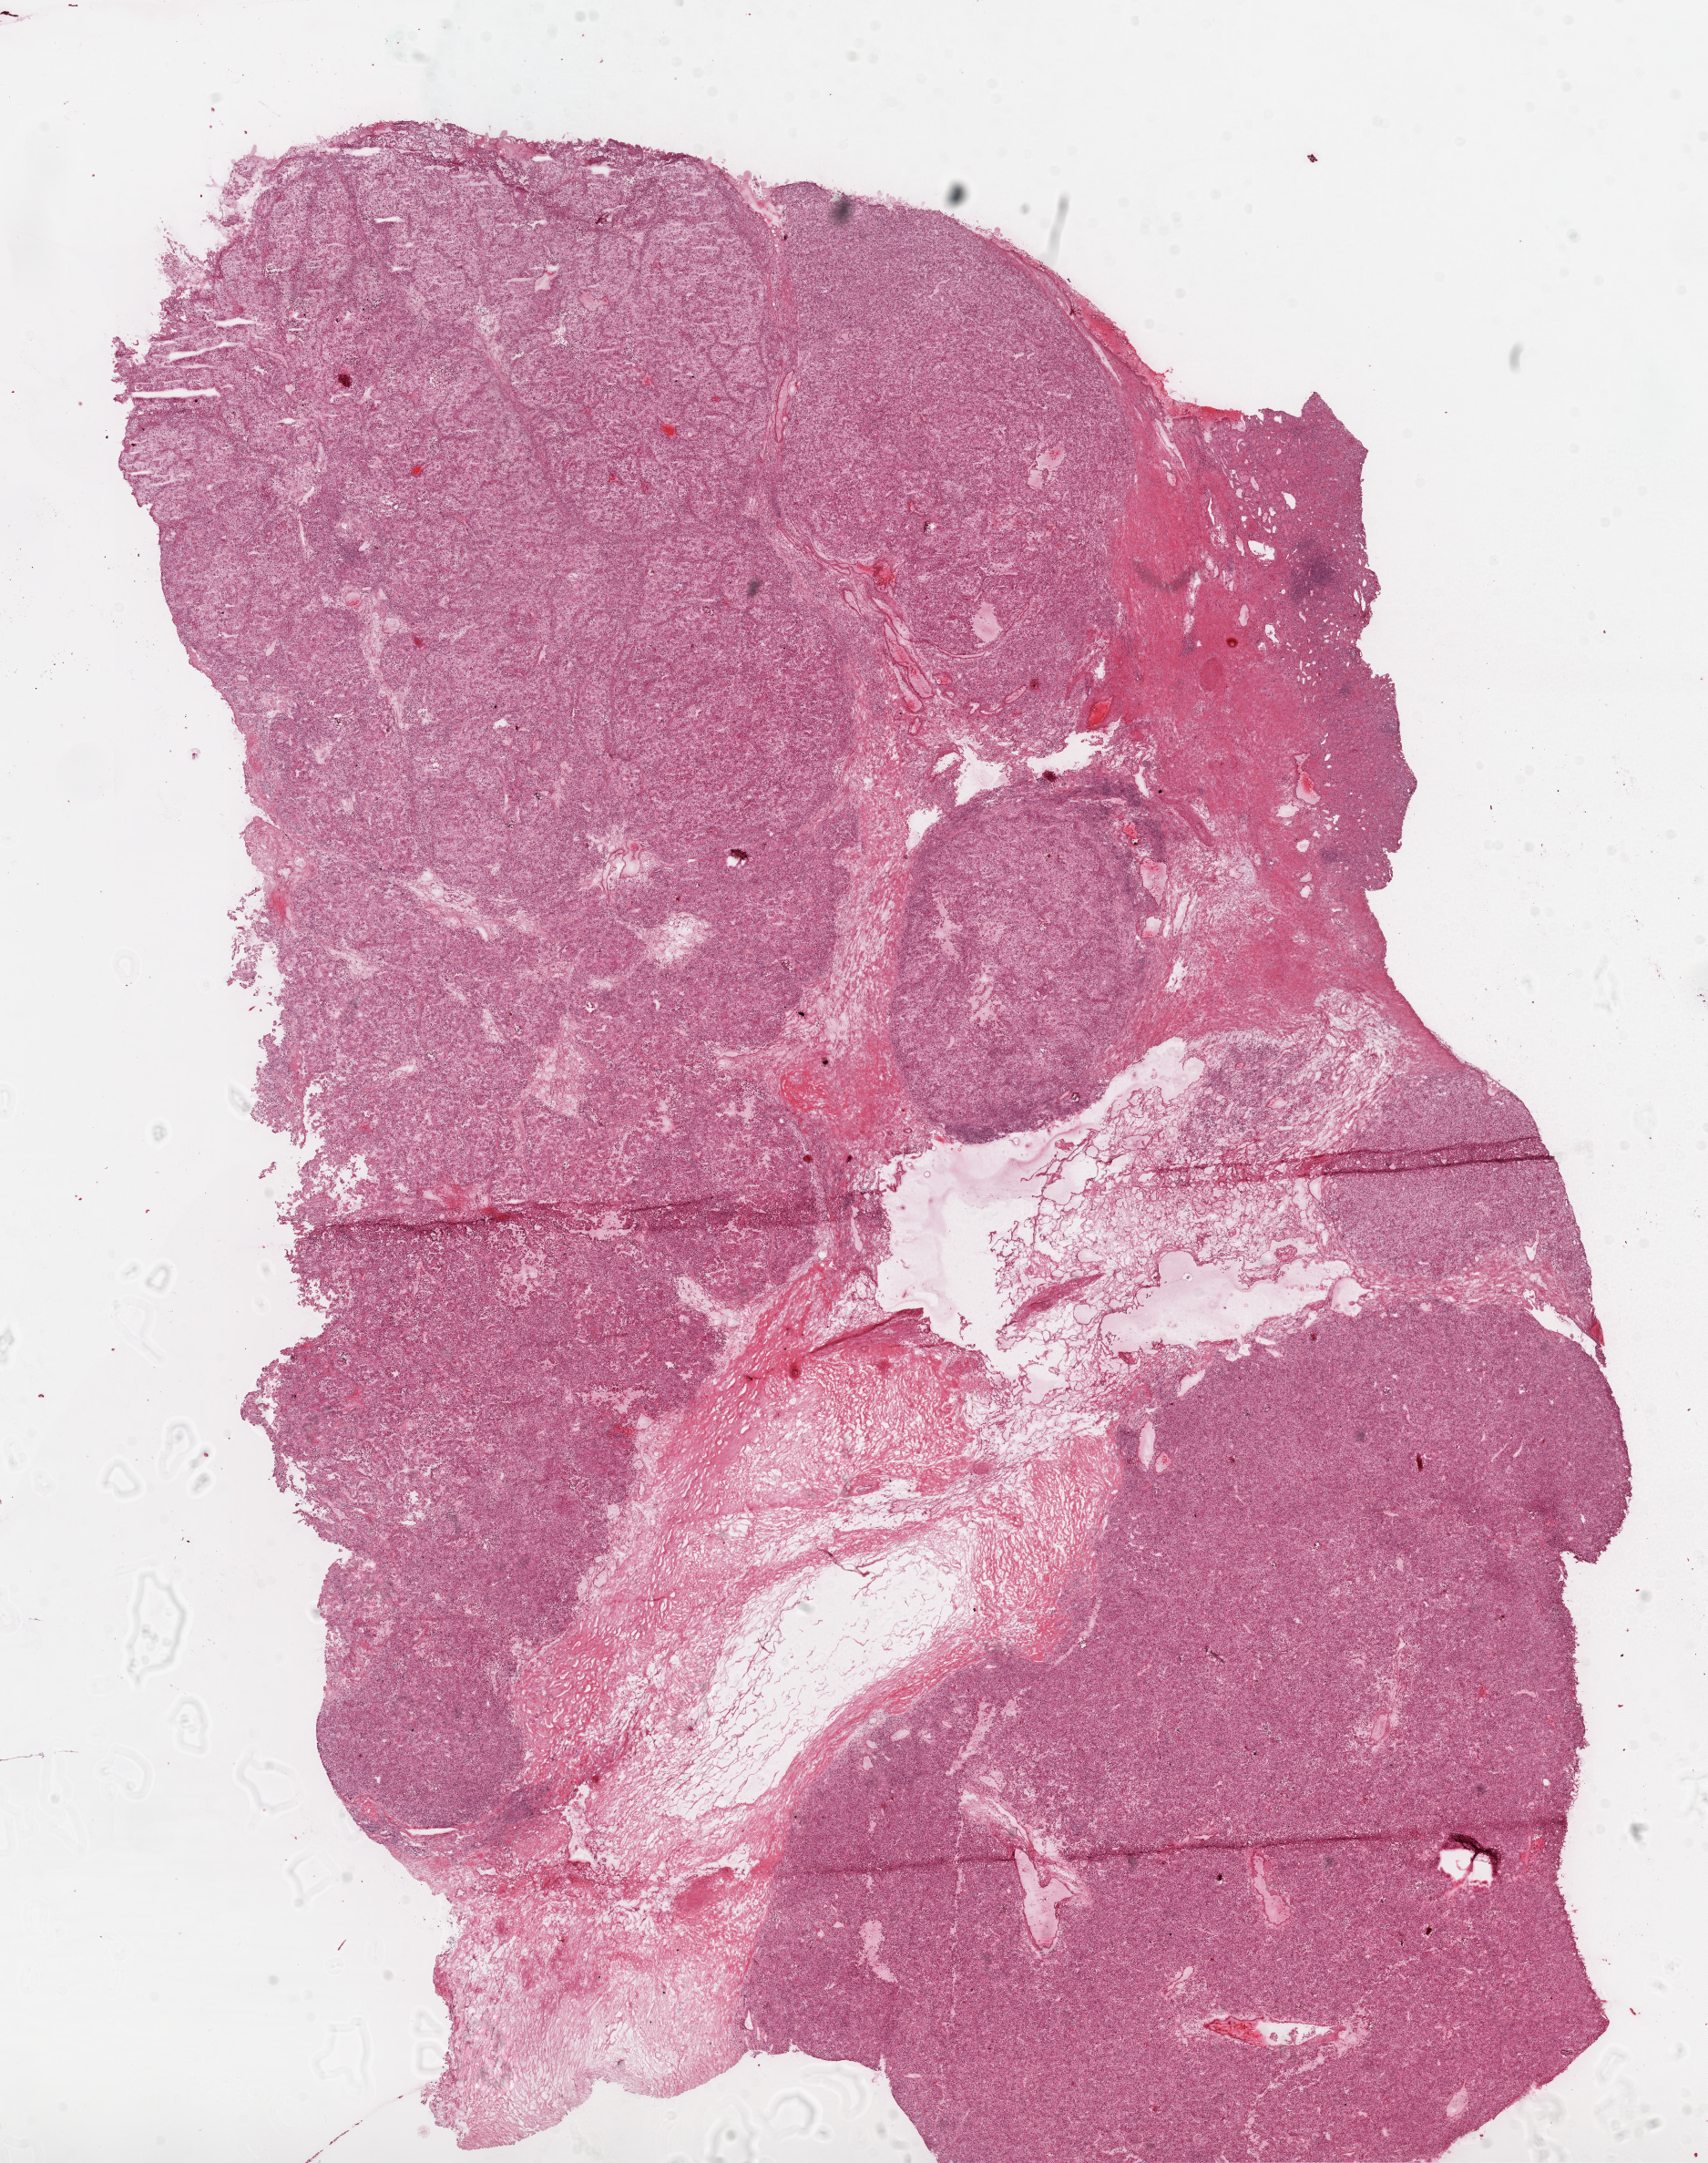
Whole-slide histology image, H&E, a low-resolution overview of the entire scanned area, about 15.0 x 19.0 mm (slide scanned at 20x). Frozen section from the top of the tissue portion. Sample: primary tumour, kidney. Male, age 57 years at initial diagnosis. Histologic grade: G3 (poorly differentiated). Composition of this section per pathologist review: tumour cells 77%, tumour nuclei 85%, normal cells 5%, stromal cells 18%, necrosis 0%.
AJCC pathologic stage: III. Laterality: right. Histologic diagnosis: Clear cell adenocarcinoma, NOS.